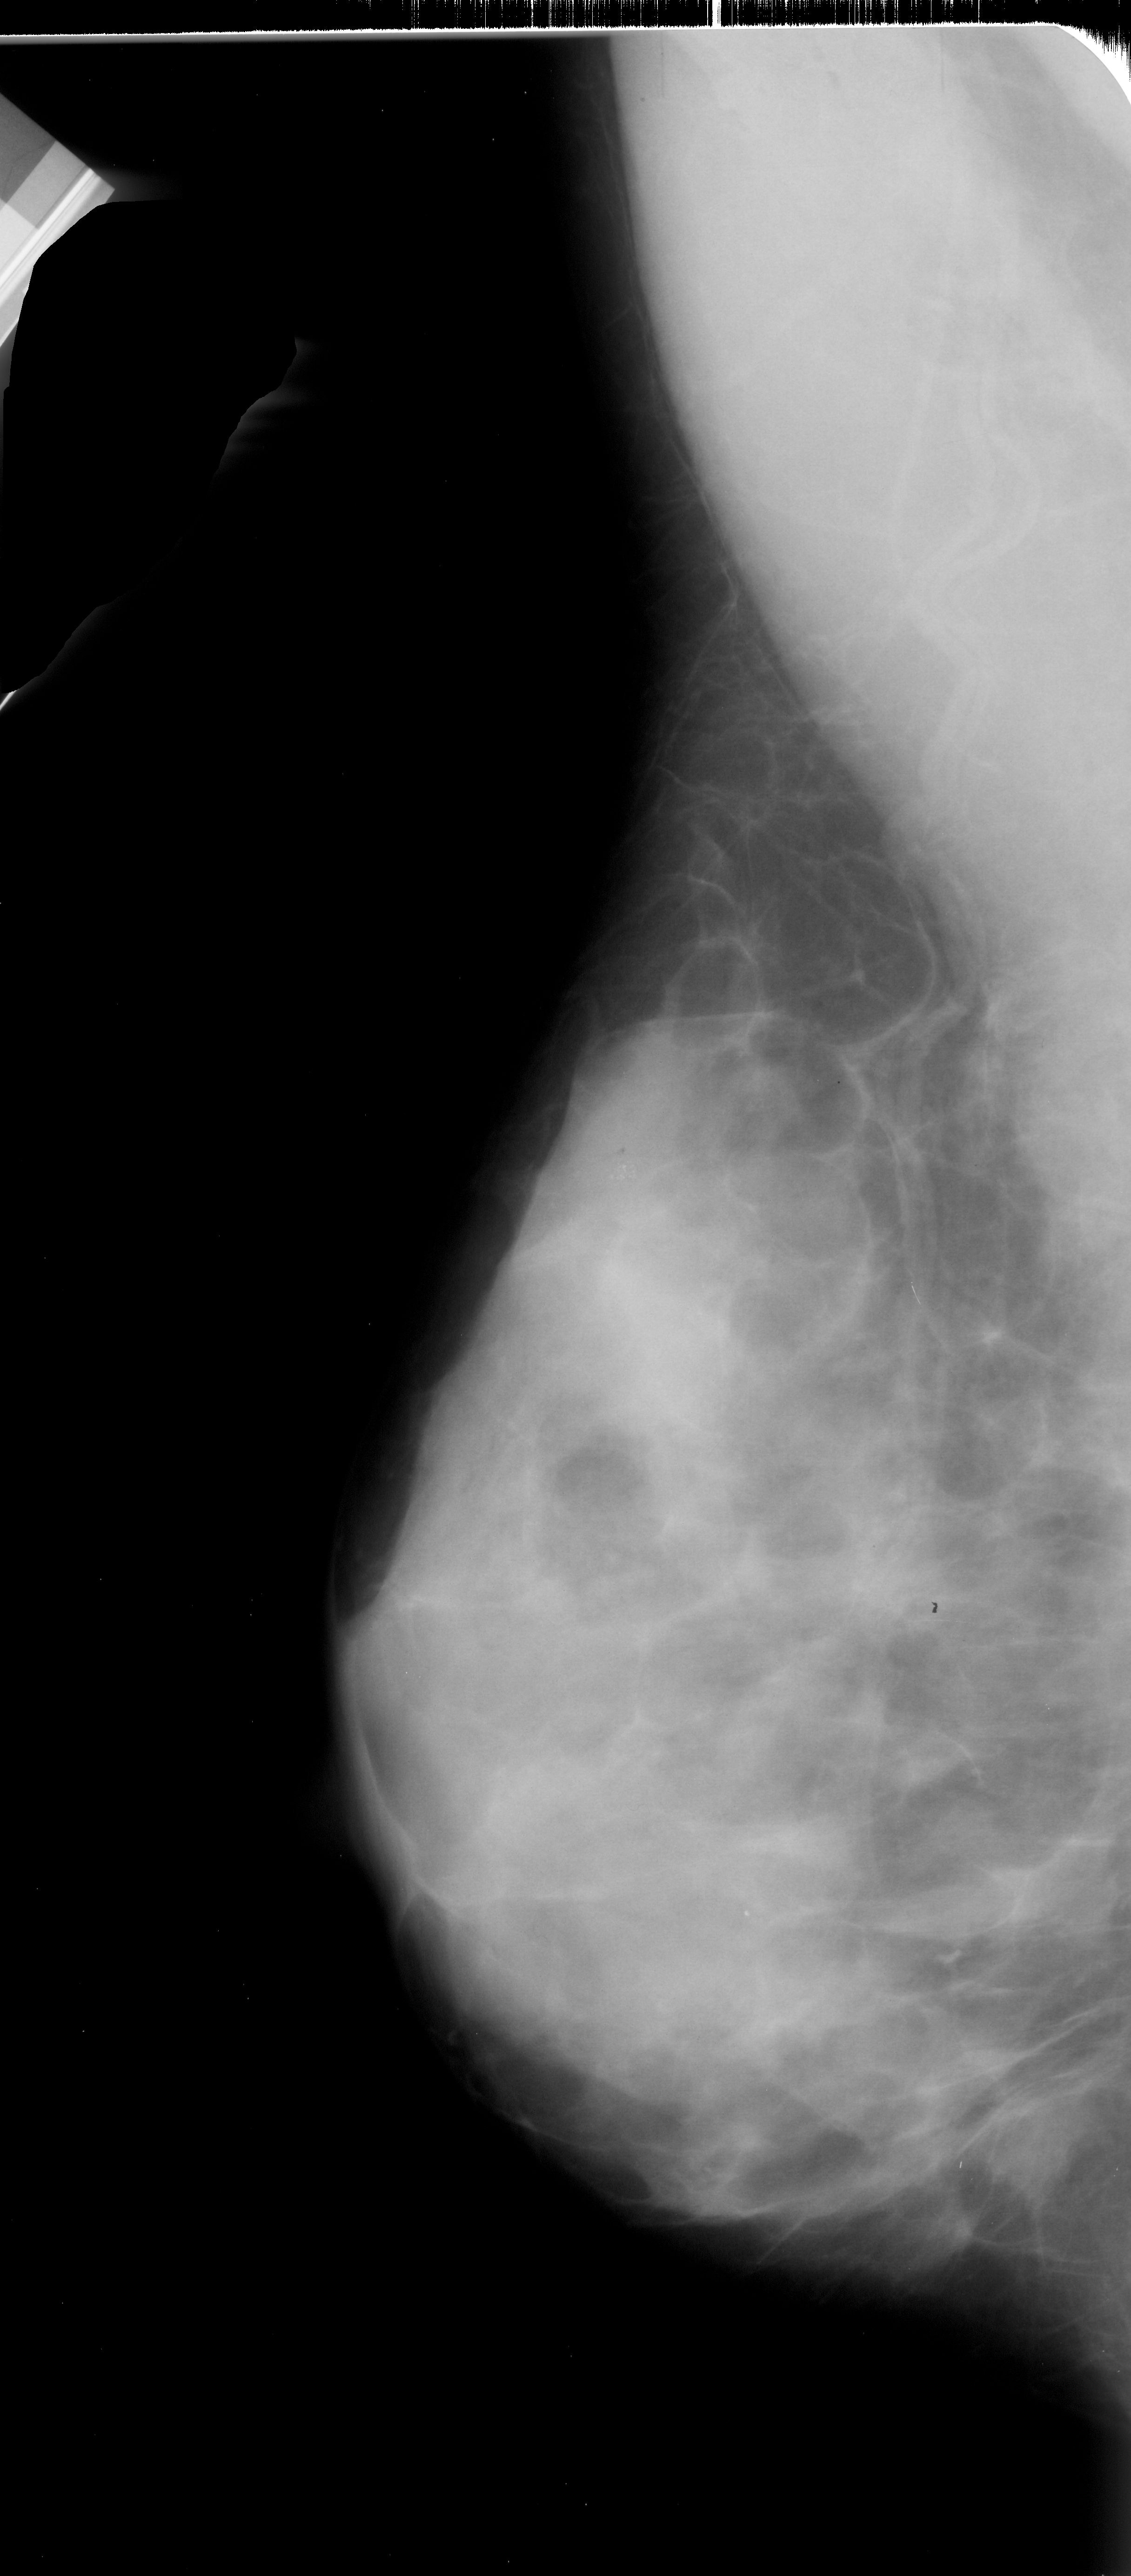
Mammogram (digitized film). Left breast. Mediolateral oblique (MLO) view. Breast composition: extremely dense (BI-RADS density category 4 of 4). 1131 × 2576 image matrix.
Expert-marked regions of interest on this image (one box per marked abnormality):
- calcifications, morphology punctate, distribution clustered; BI-RADS assessment category 4; pathology (as recorded): malignant: bounding box (x1, y1, x2, y2) in pixels: (594, 1150, 663, 1200)